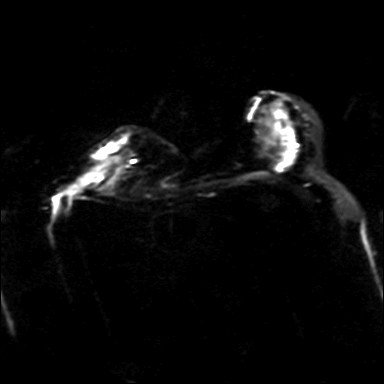
Breast MRI, one axial slice; diffusion-weighted series; image 2 of 4 stored at this slice position (different b-values; order by instance number); 3 T; 4 mm slice thickness; 384 × 384 image matrix, field of view 320 × 320 mm. Female patient.
Structures marked on this image (expert manual segmentation):
- tumour on diffusion-weighted imaging: bounding box (x1, y1, x2, y2) in pixels: (103, 148, 111, 153)